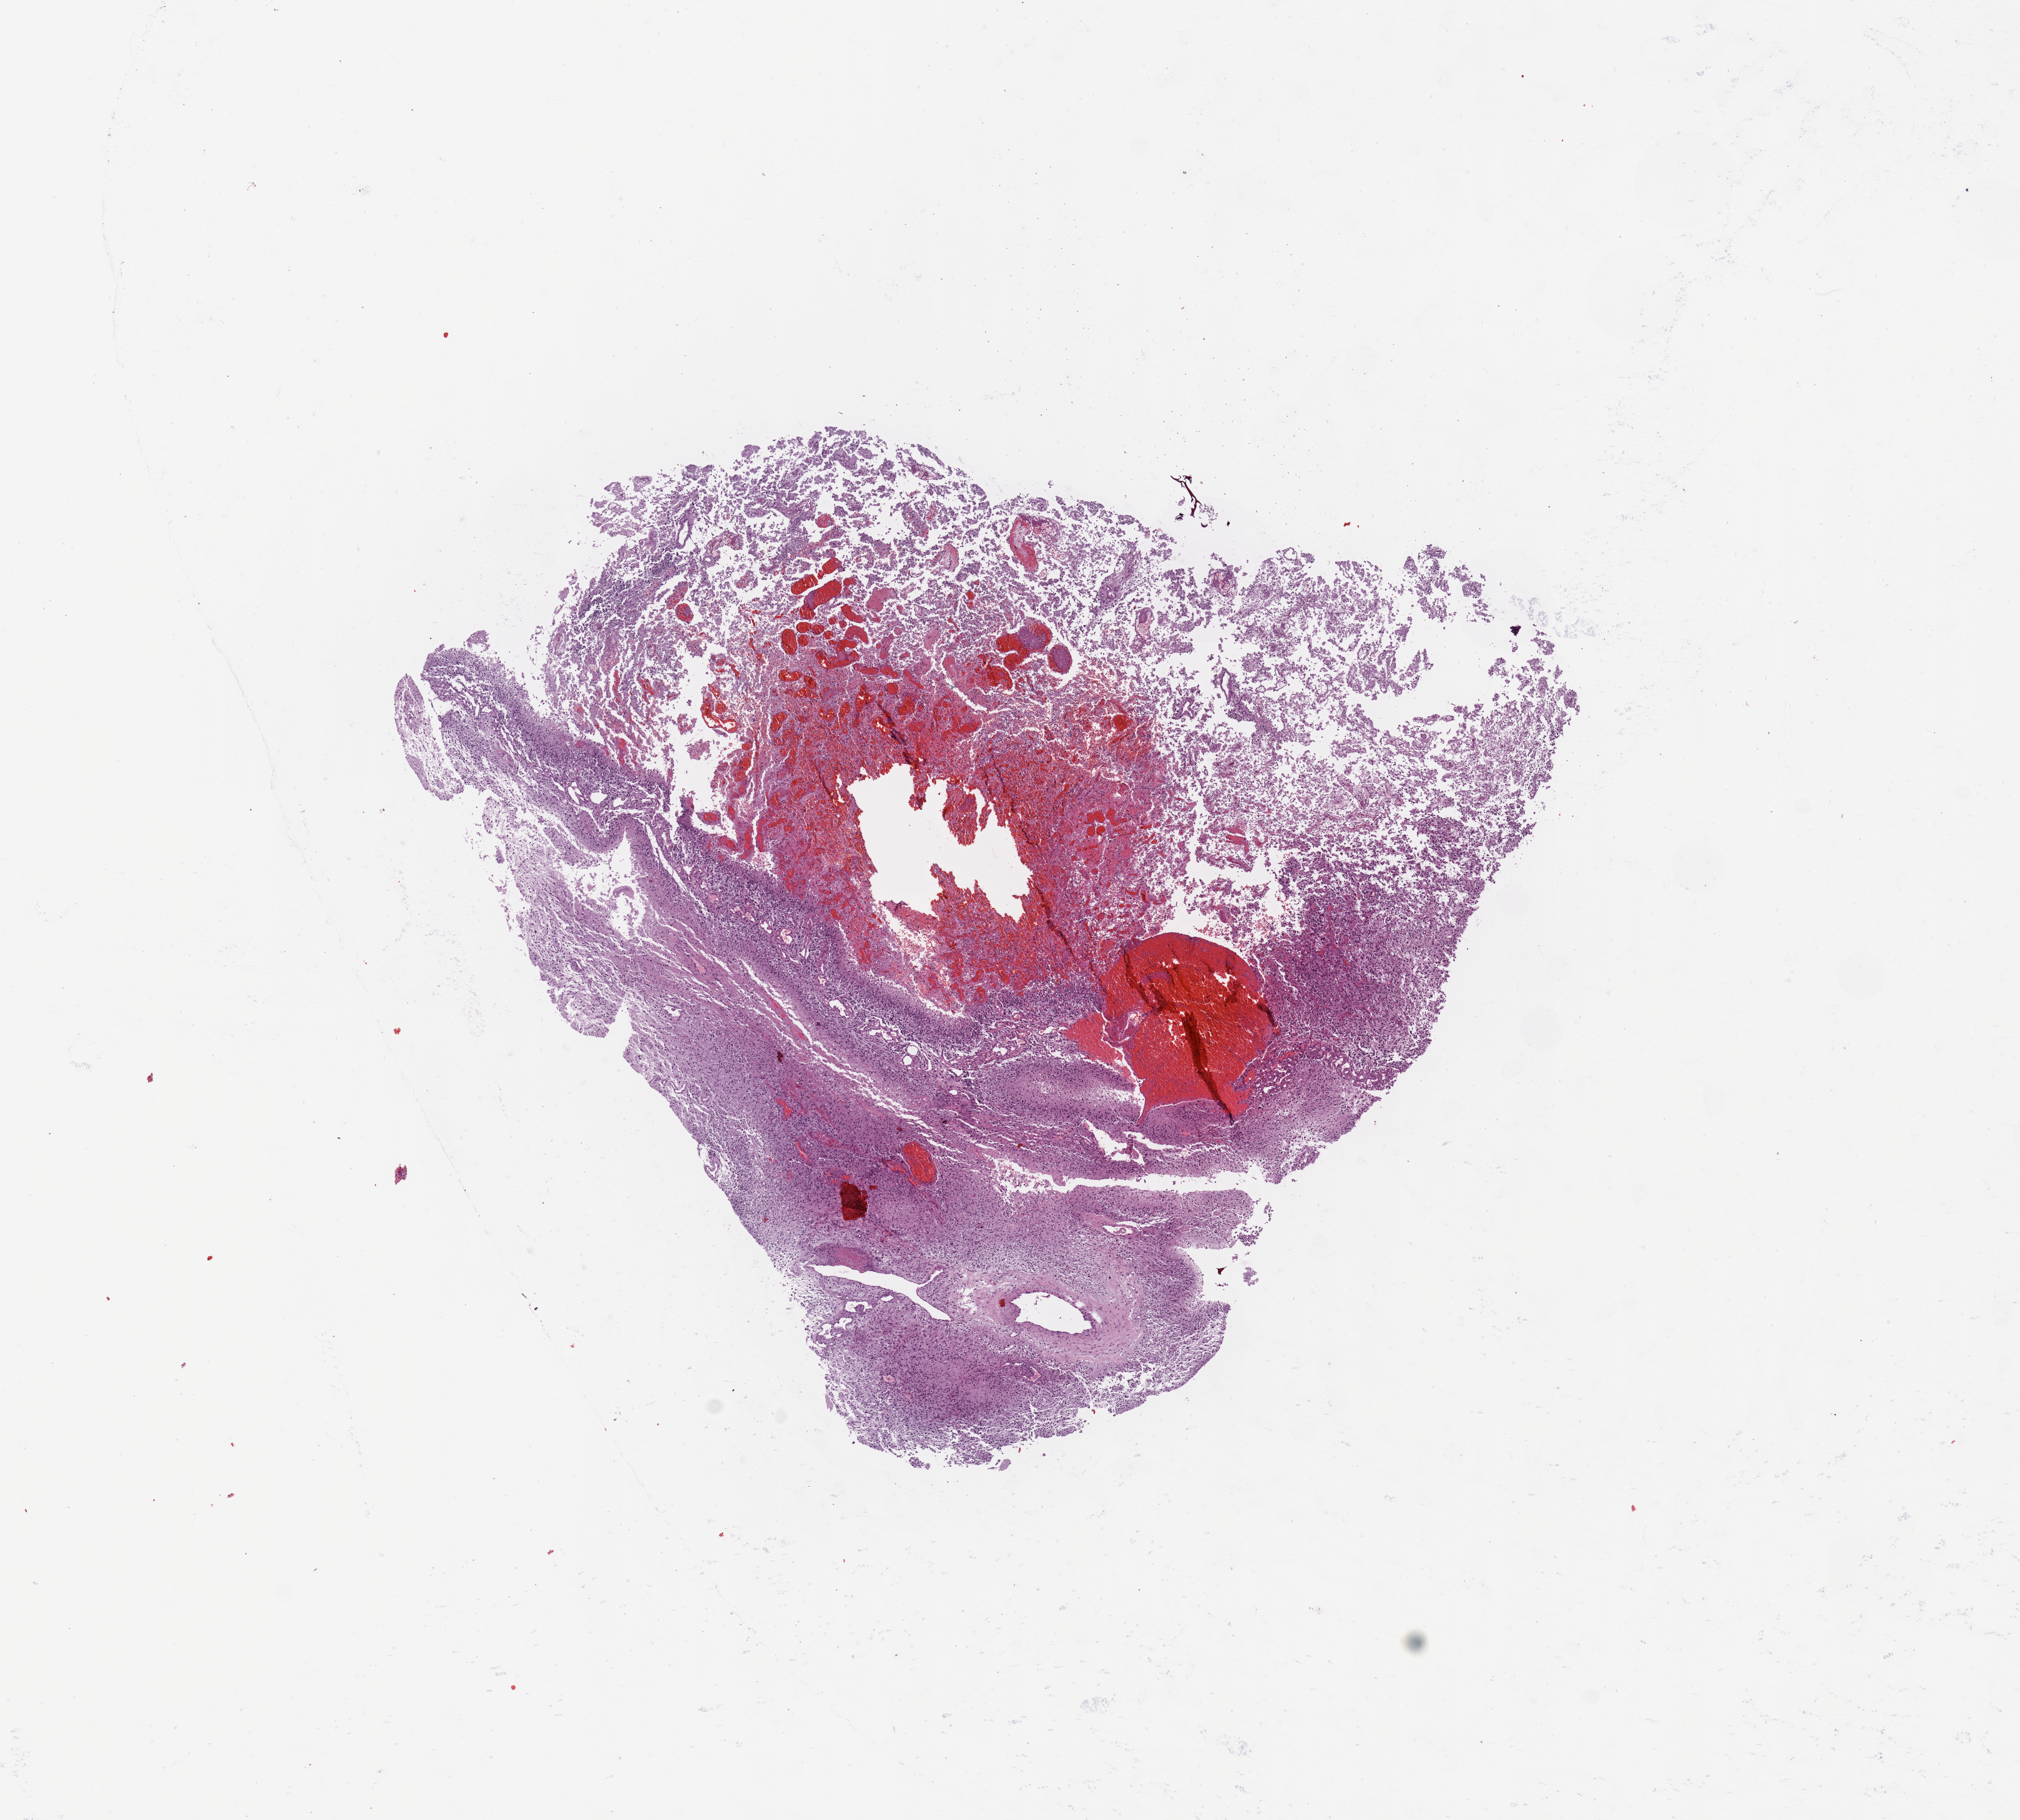
H&E-stained whole-slide image — a low-resolution overview of the entire scanned area, about 12.8 x 11.5 mm; brain, tumour tissue. Female, 54 y/o.
* histologic diagnosis: Glioblastoma